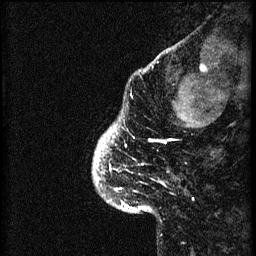
Breast MRI (dynamic contrast-enhanced), one sagittal slice. Slice 6 of 60 in the series (ordered by position). 3 images stored at this slice position (order not interpretable as contrast timing). 1.5 T. TE 4.2 ms, TR 8.2 ms. 2 mm slice thickness. 256 × 256 image matrix, field of view 180 × 180 mm. Female patient, age 41 years.
Structures marked on this image (semi-automatic segmentation, software-assisted and operator-edited):
- analysis volume of interest (the breast-tissue region the enhancement analysis was run in; not a lesion): bounding box [x1, y1, x2, y2] px = [95, 116, 174, 205]
- tumour enhancement mask (voxels above the 70 % enhancement threshold inside the analysis volume of interest): [95, 128, 167, 191]